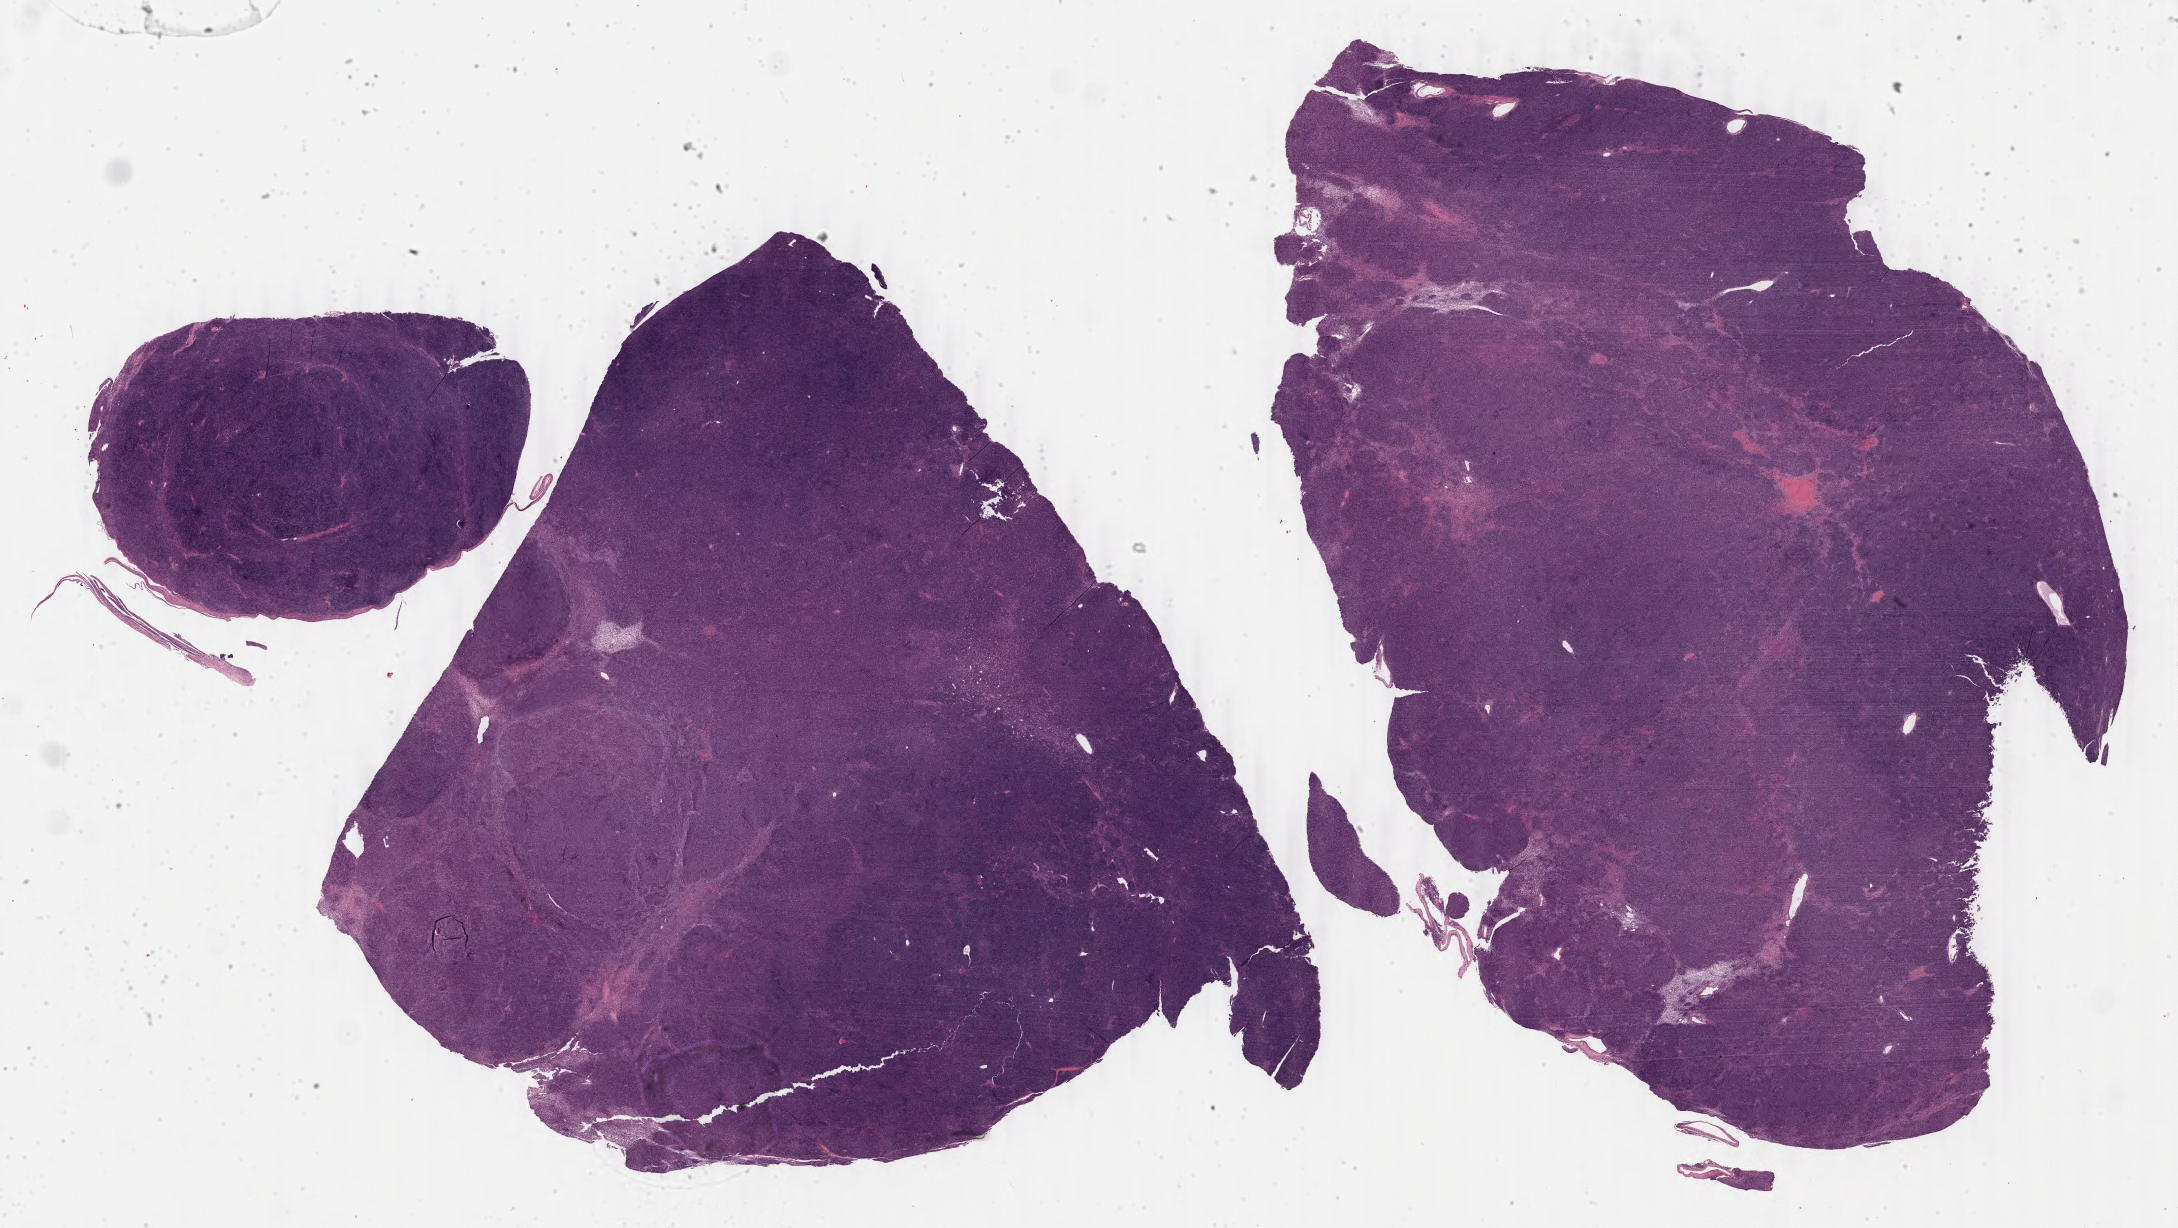
Whole-slide histology image, H&E — whole scanned area (about 34.4 x 19.4 mm, acquisition: 40x scan) shown as a low-resolution overview. Formalin-fixed paraffin-embedded (FFPE) diagnostic section. Sample: primary tumour, thymus. Female, age 72 years at initial diagnosis.
Pathologic diagnosis: Thymoma, type AB, malignant.